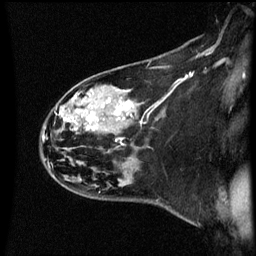
Breast MRI (dynamic contrast-enhanced), one sagittal slice; slice 40 of 60 in the series (ordered by position); dynamic contrast-enhanced series, image 2 of 3 at this slice position (ordered by acquisition); 1.5 T; TE 4.2 ms, TR 8.9 ms; 2 mm slice thickness; 256 × 256 image matrix. Patient: female, 44 years. Case-level facts recorded for this patient, not image findings: setting: breast cancer imaged before/during neoadjuvant chemotherapy; receptor status: HR-positive, HER2-negative.
Structures marked on this image (semi-automatic segmentation, software-assisted and operator-edited):
- analysis volume of interest (the breast-tissue region the enhancement analysis was run in; not a lesion): box from (x=43, y=78) to (x=151, y=189) px
- tumour enhancement mask (voxels above the 70 % enhancement threshold inside the analysis volume of interest): (x=86, y=100)–(x=121, y=131)